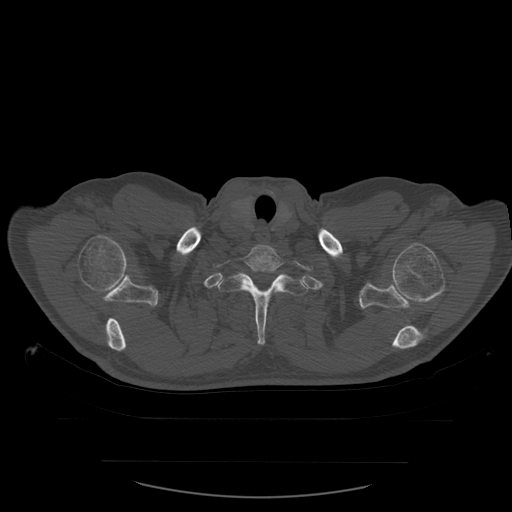
CT including the spine, one axial slice; slice 480 of 590 in the series (ordered by position); bone window (W 1800 / L 400 HU); 1.25 mm slice thickness; 512 × 512 image matrix. Patient age 71 years. From the clinical record (not read from this slice): primary cancer: lung.
Outlined on this slice (semi-automatic segmentation, software-assisted and operator-edited):
- T1 vertebra: box from (x=216, y=246) to (x=313, y=289) px
- T2 vertebra: (x=217, y=273)–(x=310, y=345)